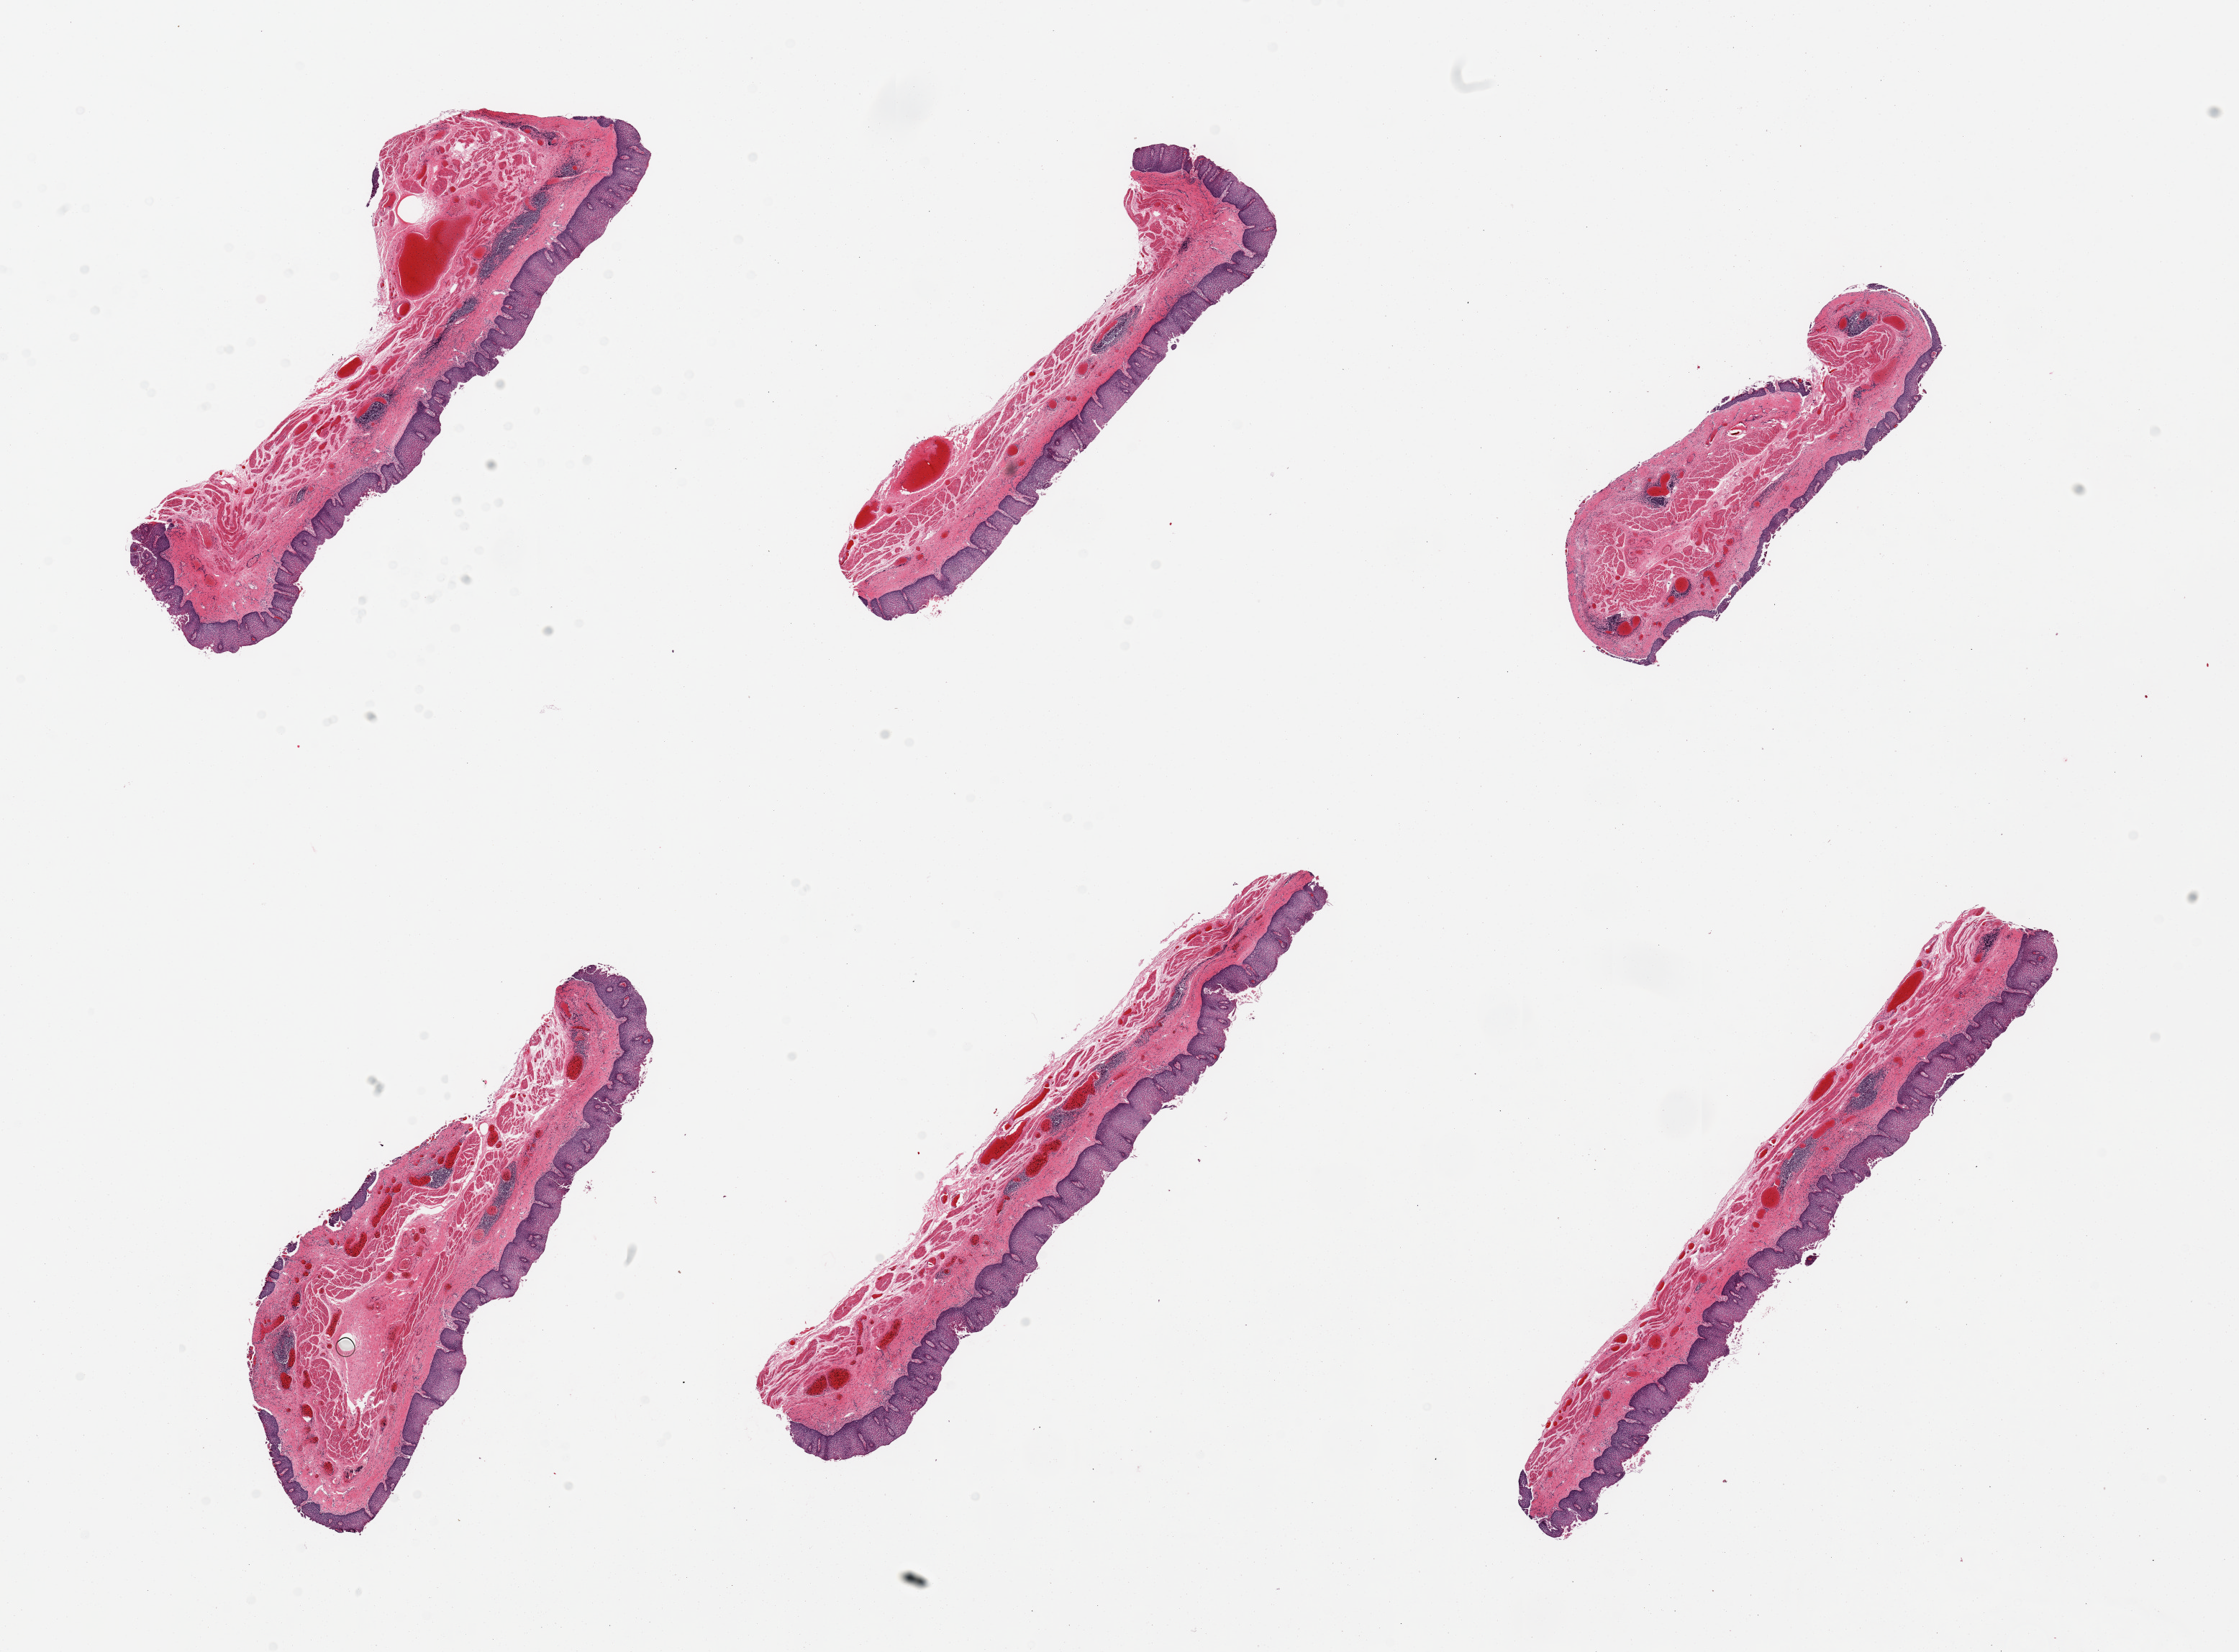
Whole-slide image, H&E stain, brightfield — whole scanned area (about 24.6 x 18.2 mm, slide scanned at 20x) shown as a low-resolution overview. PAXgene-fixed paraffin-embedded (PFPE) section. Section of esophageal mucous membrane (target tissue). Tissue donor sample. Male donor.
Review note (as recorded): 6 pieces, squamous mucosa is ~0.3mm, 20-25% thickness.